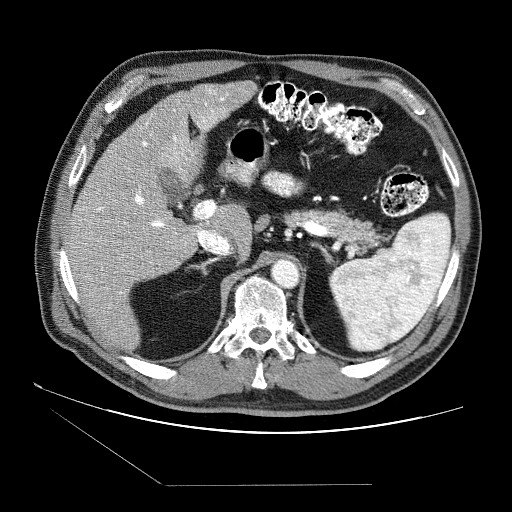
Contrast-enhanced abdominal CT (liver protocol), one axial slice; slice 47 of 87 in the series (ordered by position); reconstruction kernel STANDARD; 120 kVp; soft-tissue window (W 400 / L 40 HU); 2.5 mm slice thickness; 512 × 512 image matrix, field of view 400 × 400 mm. From the clinical record (not read from this slice): diagnosis: hepatocellular carcinoma (patient treated with transarterial chemoembolisation; whether this scan precedes or follows treatment is not stated here); TNM stage (as recorded): Stage-II; Child-Pugh class: B; tumour differentiation: no biopsy; tumour size: 2.6 cm.
Structures marked on this image (semi-automatic segmentation, software-assisted and operator-edited):
- liver parenchyma outside the tumour (the mass and vessels are separate outlines, so this box may not span the whole liver): bounding box [x1, y1, x2, y2] px = [64, 82, 255, 349]
- liver vessels: [74, 90, 228, 308]